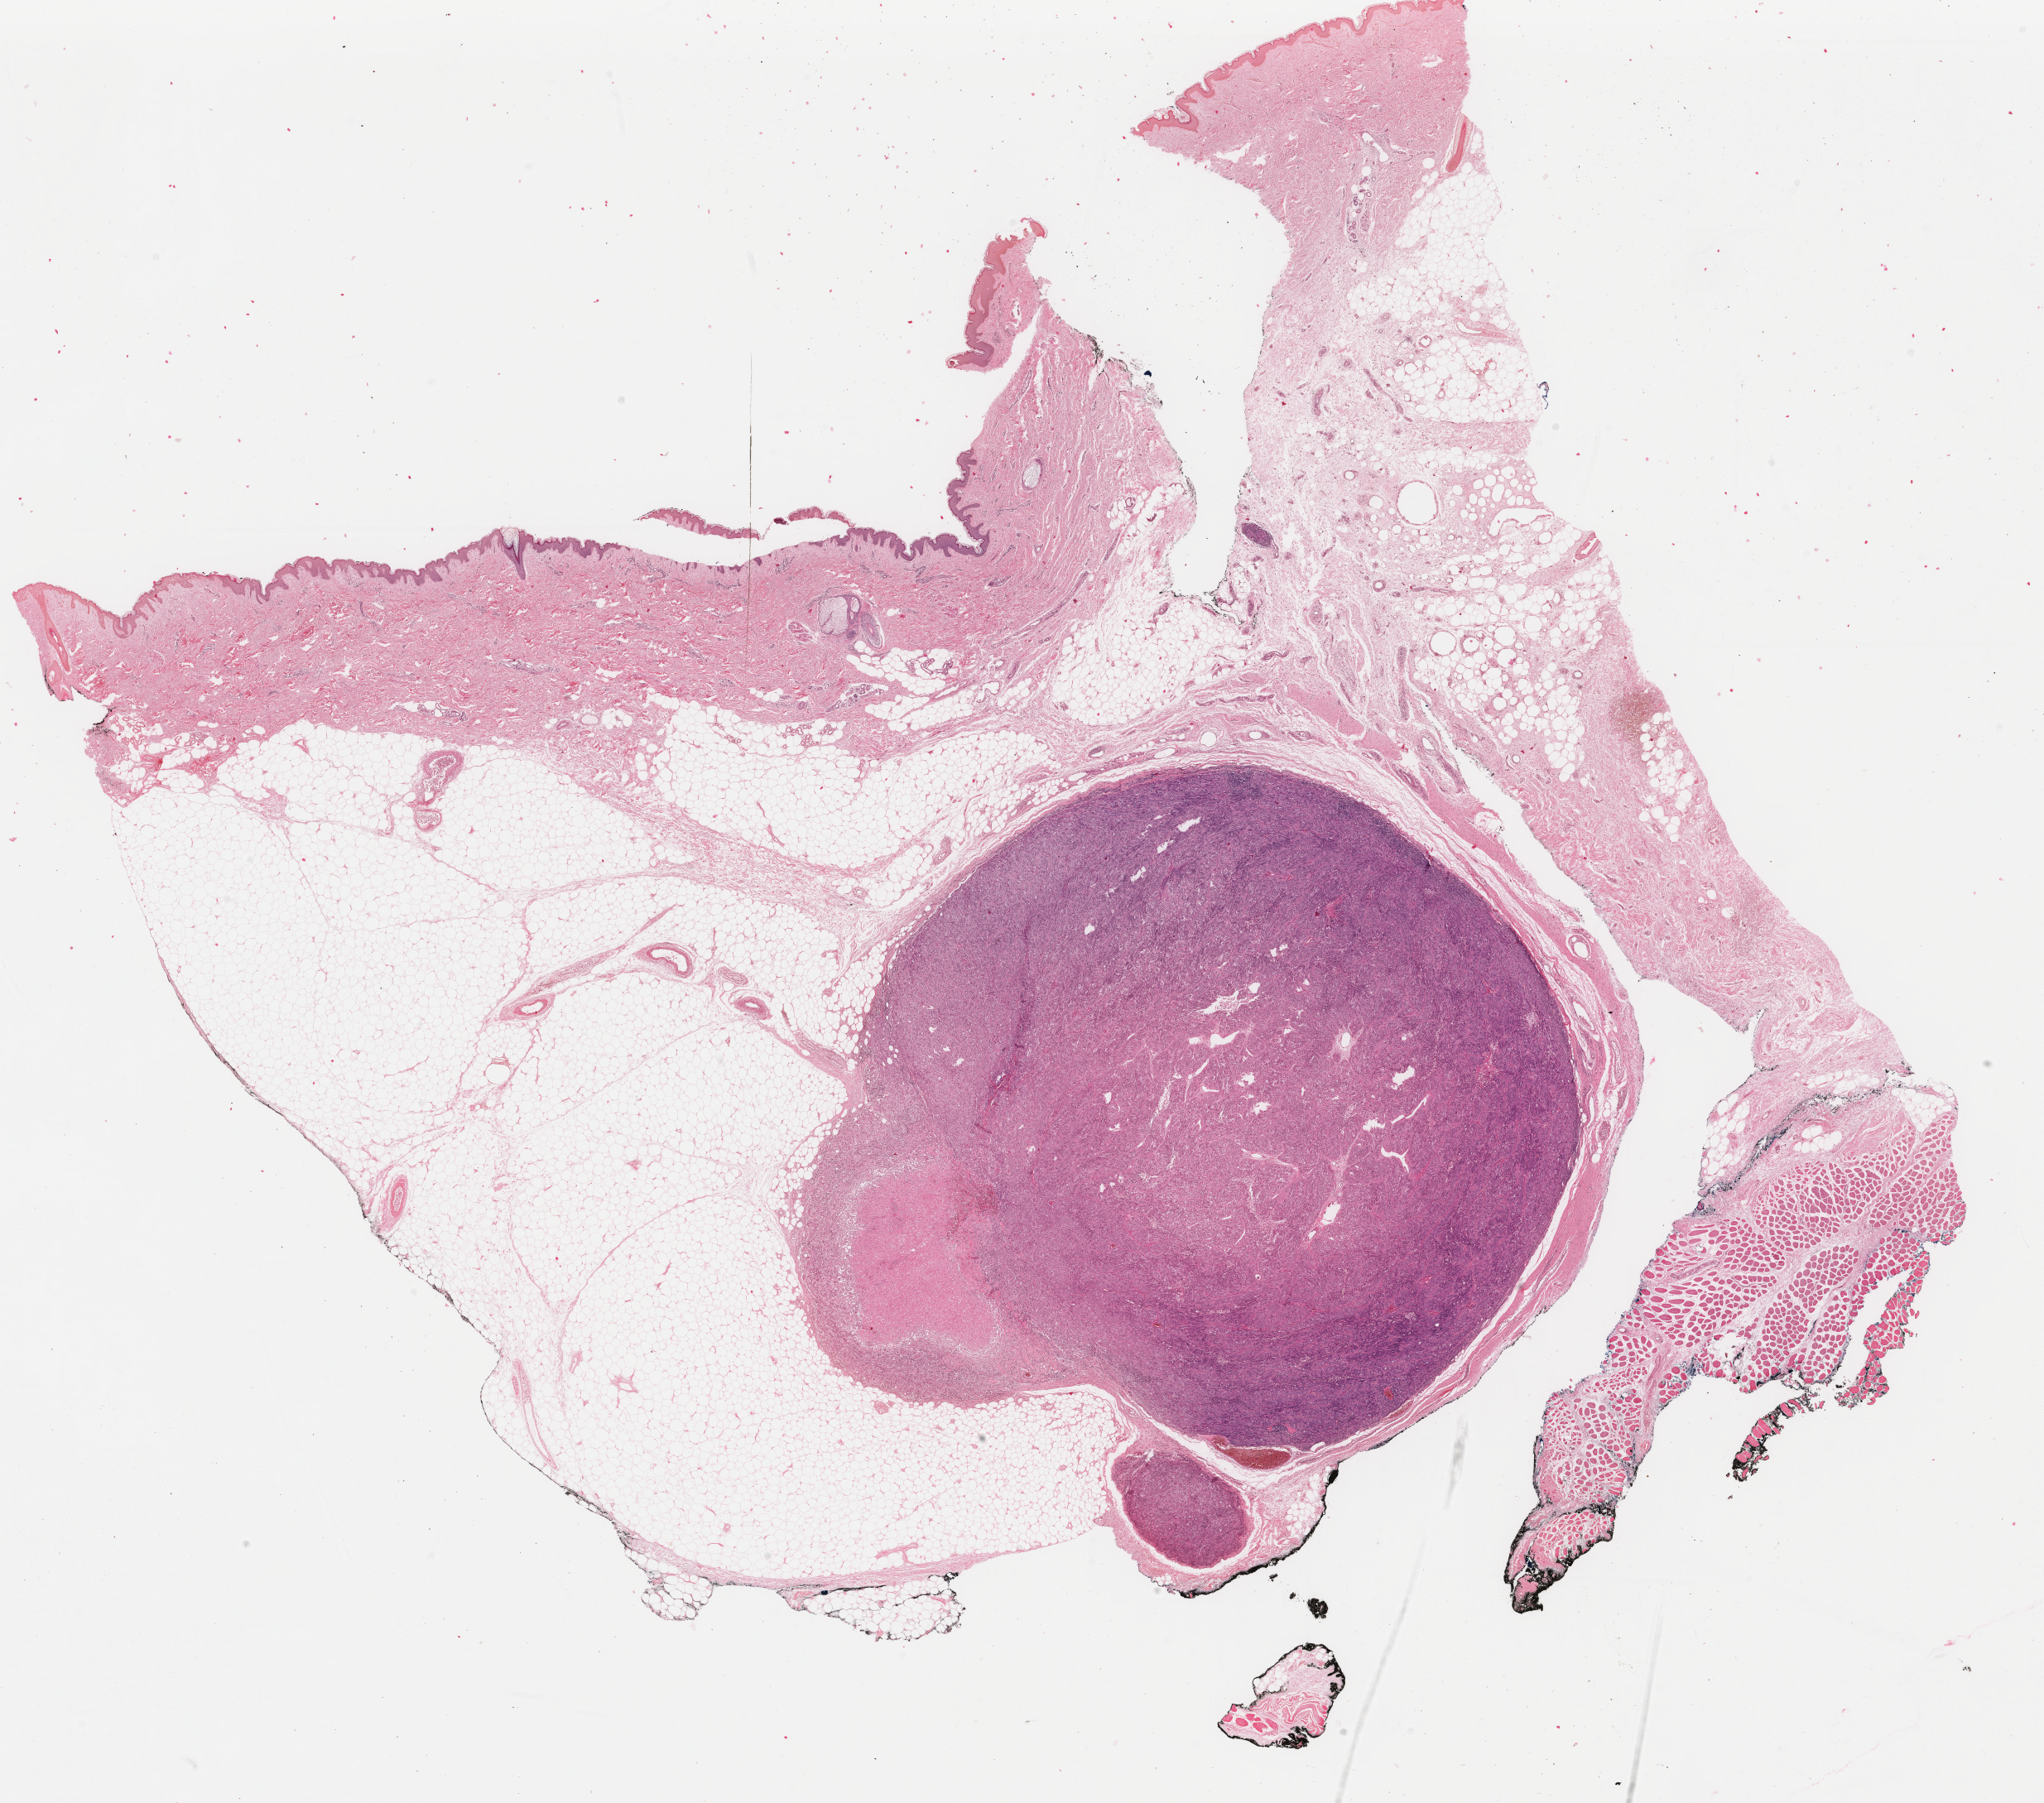
Digitized H&E-stained tissue section (whole slide) — a low-resolution overview of the entire scanned area, about 19.6 x 17.3 mm (slide scanned at 40x). Formalin-fixed paraffin-embedded (FFPE) diagnostic section. Sample: primary tumour, skin. Male, age 51 years at initial diagnosis.
Diagnosis: Malignant melanoma, NOS.